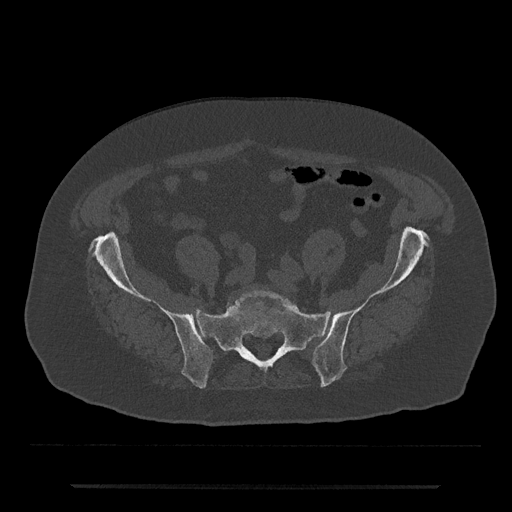
CT including the spine, one axial slice; position 237 of 797 along the scan axis; reconstruction kernel Br40s/3; 120 kVp; bone window (W 1800 / L 400 HU); 0.5 mm slice thickness; 512 × 512 image matrix. Patient: male, 80 years. From the clinical record (not read from this slice): primary cancer: prostate; vertebrae with lytic lesions (as recorded): L1, T11.
Structures marked on this image (semi-automatic segmentation, software-assisted and operator-edited):
- L5 vertebra: bounding box (x1, y1, x2, y2) in pixels: (233, 290, 298, 311)